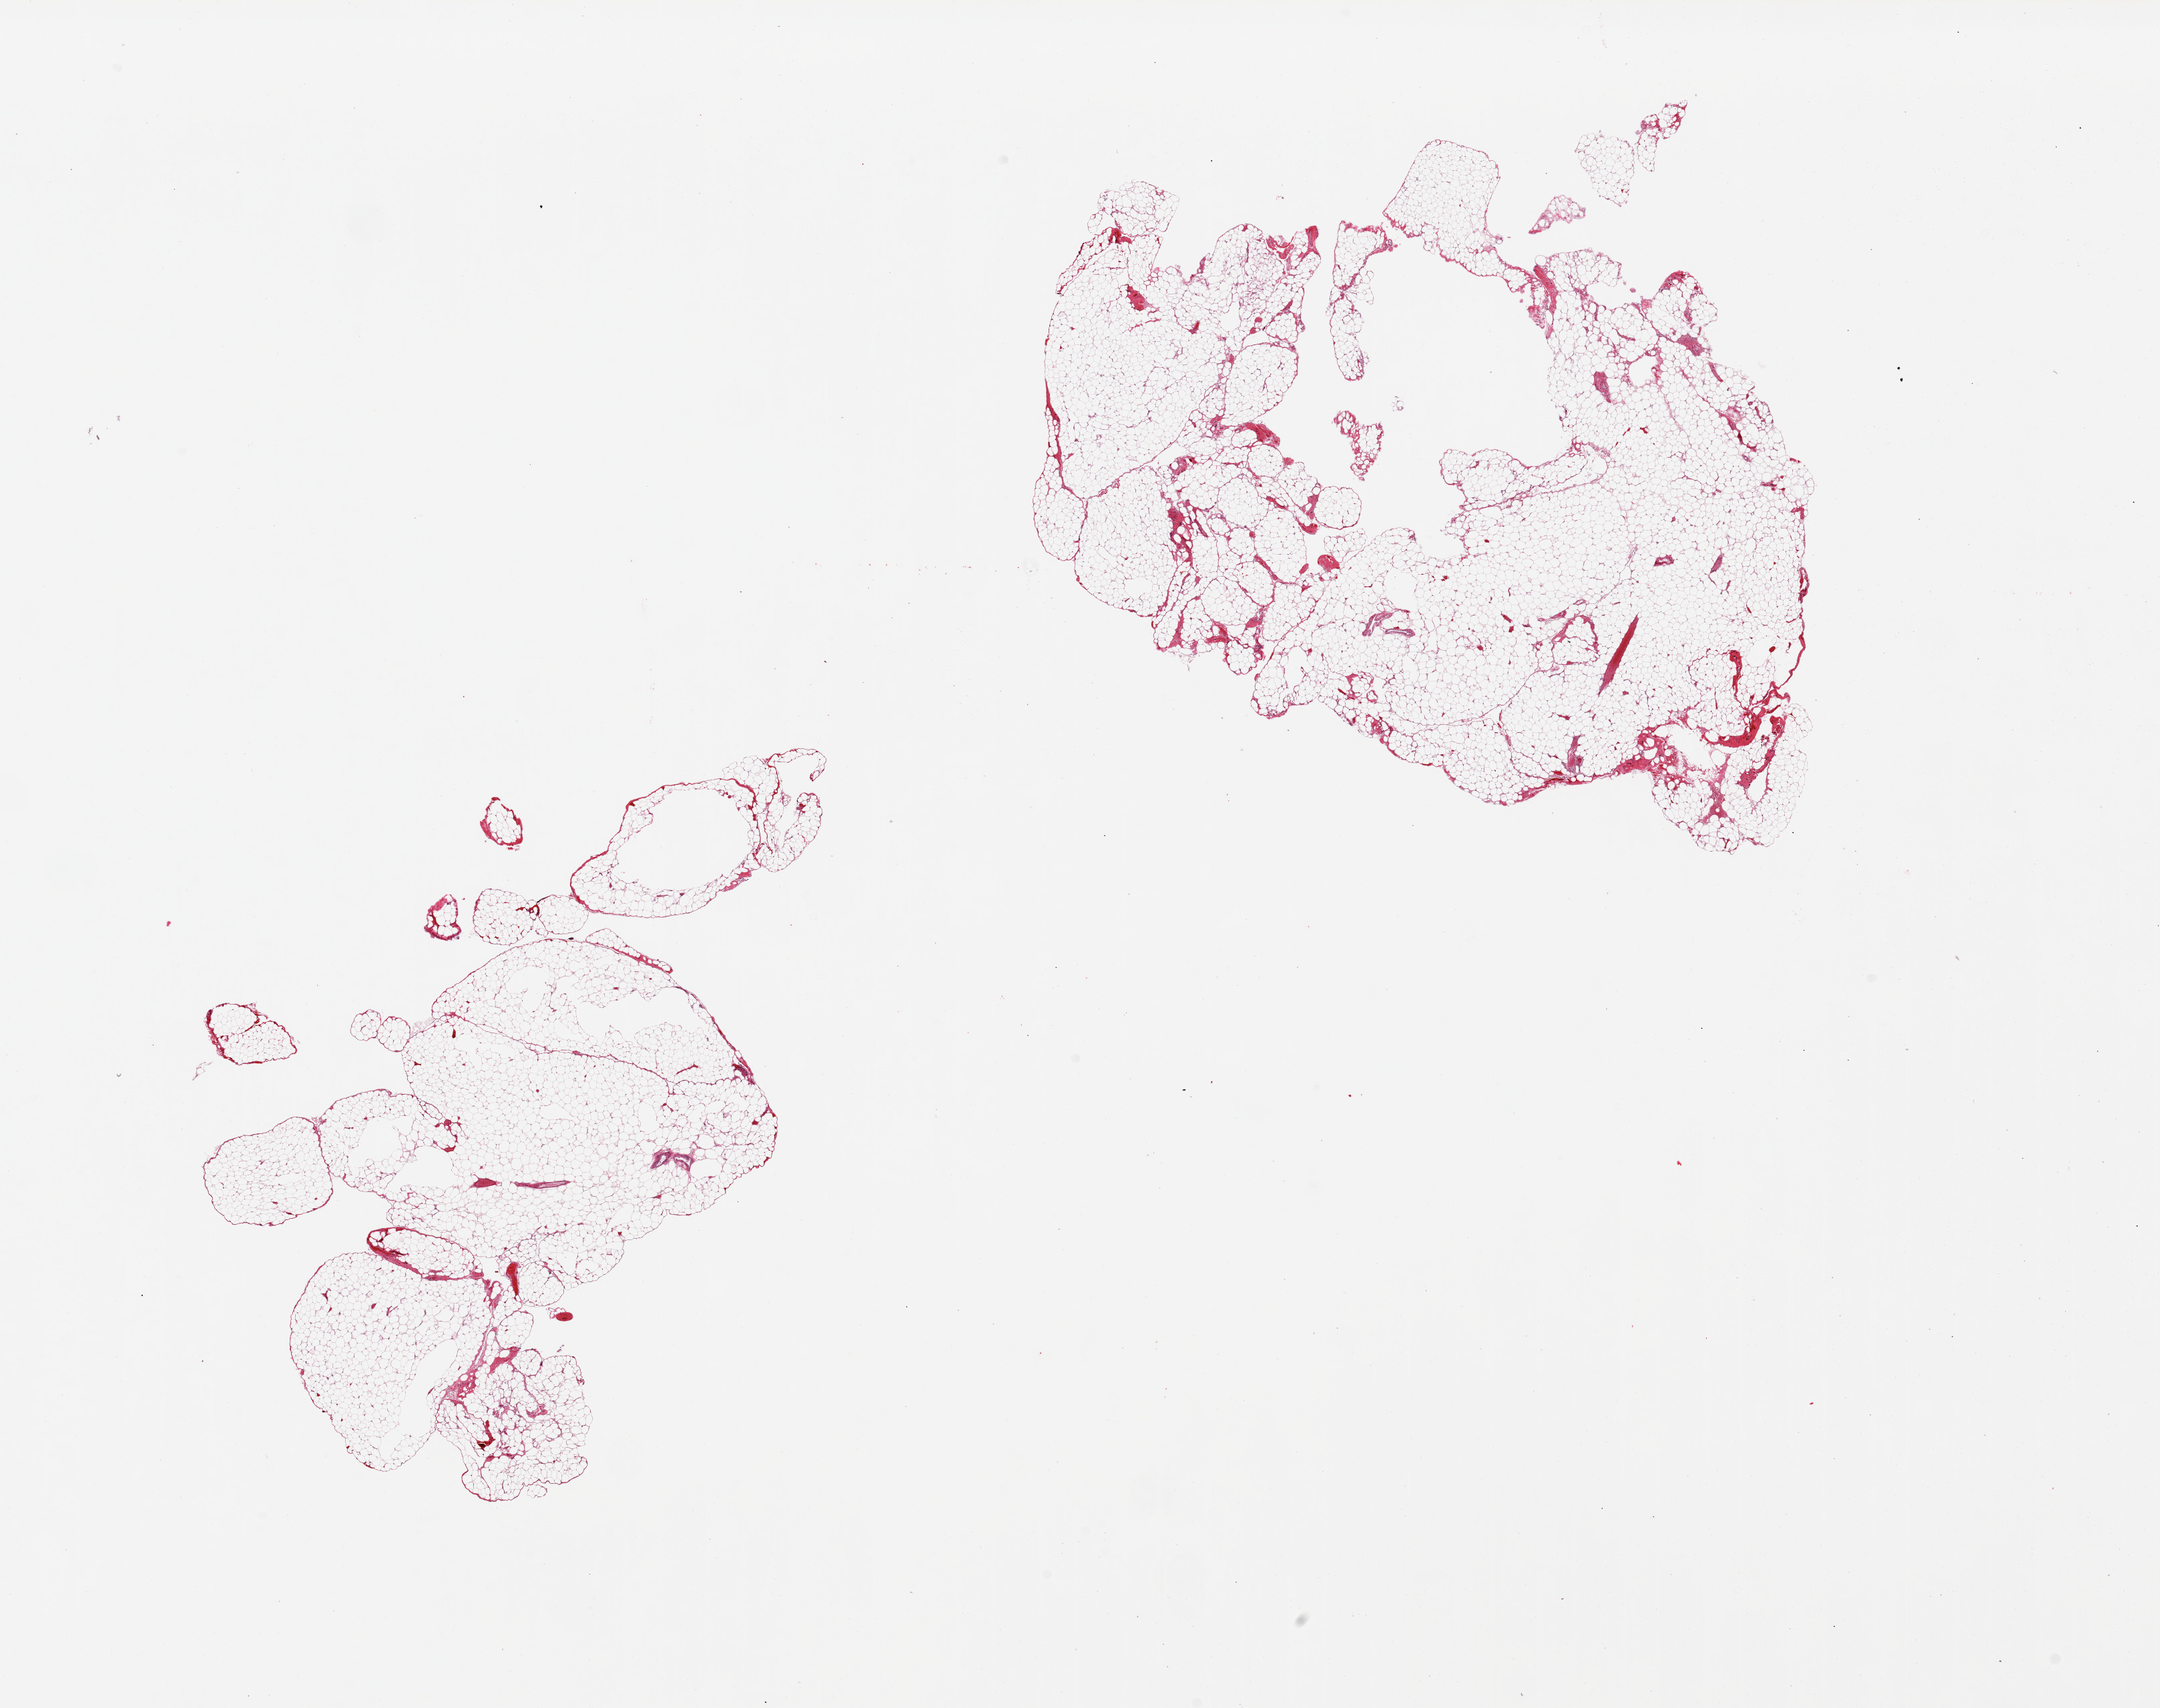
H&E whole-slide image, brightfield — shown as a low-resolution overview of the whole scanned area (about 25.6 x 20.2 mm, from a 20x scan); PAXgene-fixed, paraffin-embedded tissue; sampled site (target tissue): omentum; tissue donor sample.
Reviewer comment on this tissue sample: 2 pieces ~10% interstitial vessels.